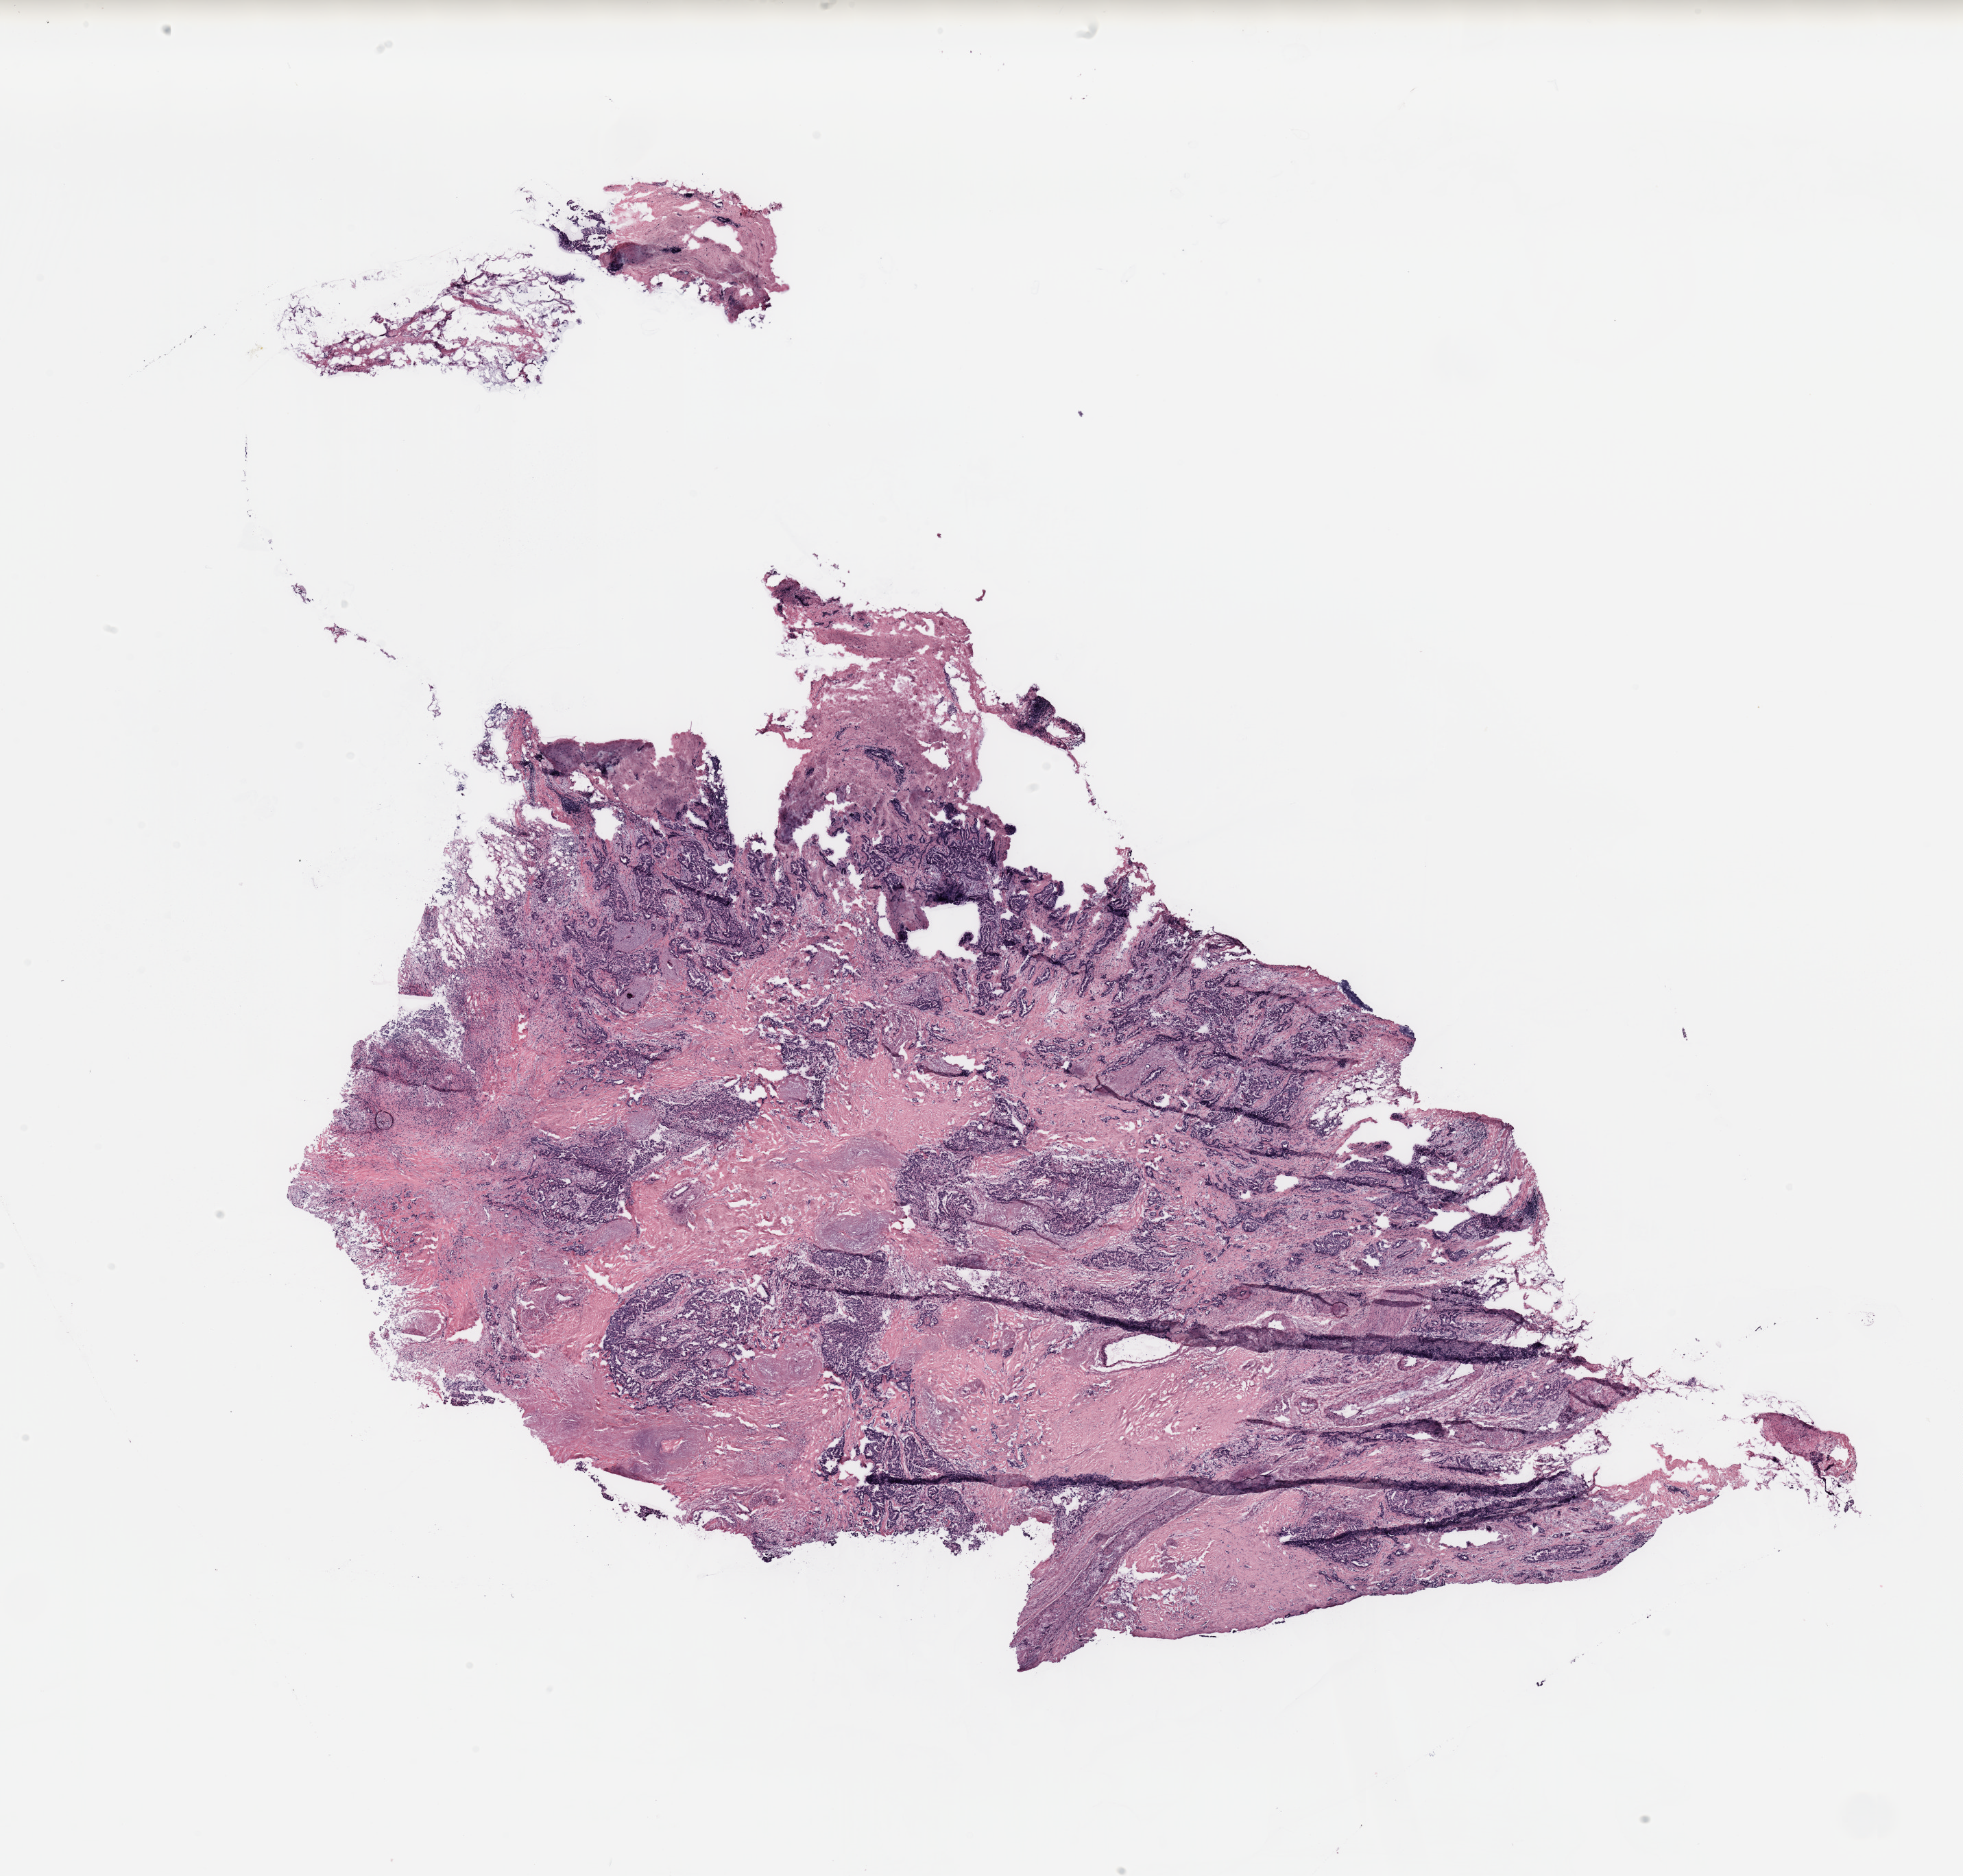
Digitized H&E tissue section (whole slide) — whole scanned area (about 22.6 x 21.6 mm, acquisition: 20x scan) shown as a low-resolution overview, breast, tissue type not recorded.
• patient diagnosis (cohort enrolment): breast cancer (breast)